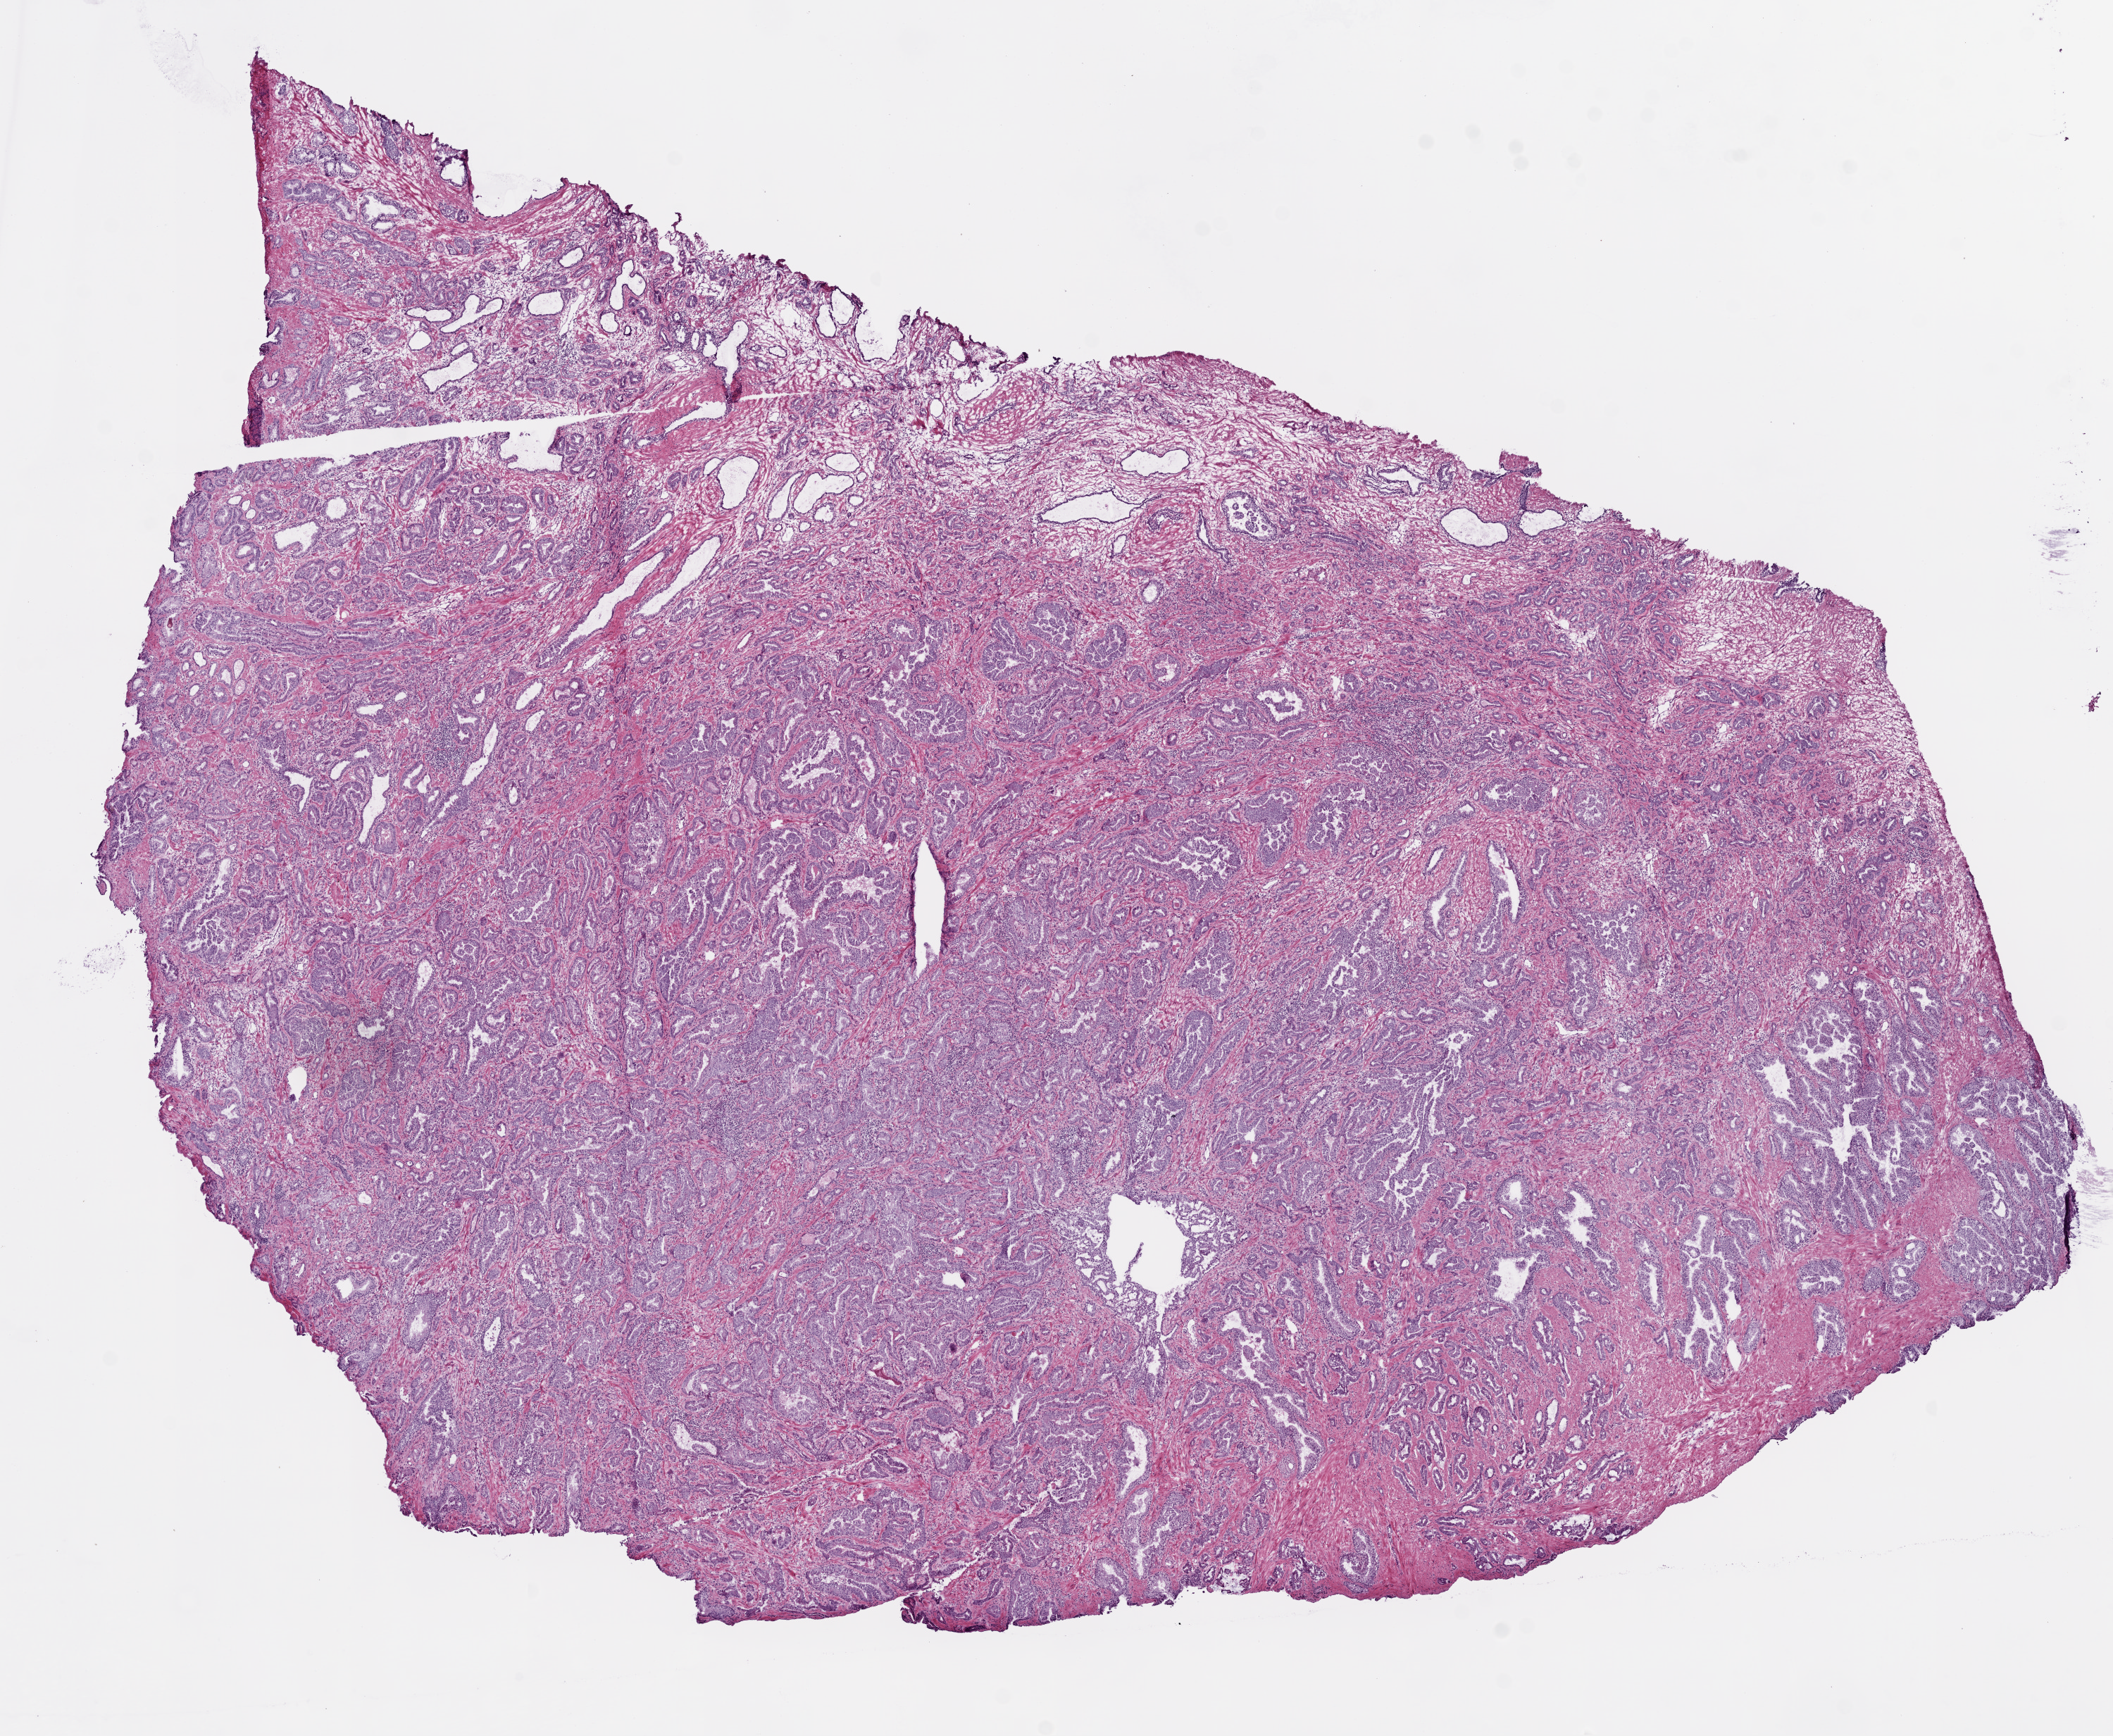
H&E-stained whole-slide image — a low-resolution overview of the entire scanned area, about 12.0 x 9.9 mm (from a 20x scan); frozen section from the top of the tissue portion; sample: primary tumour, prostate. Male, age 51 years at initial diagnosis.
Diagnosis: Acinar cell carcinoma (prostate gland).